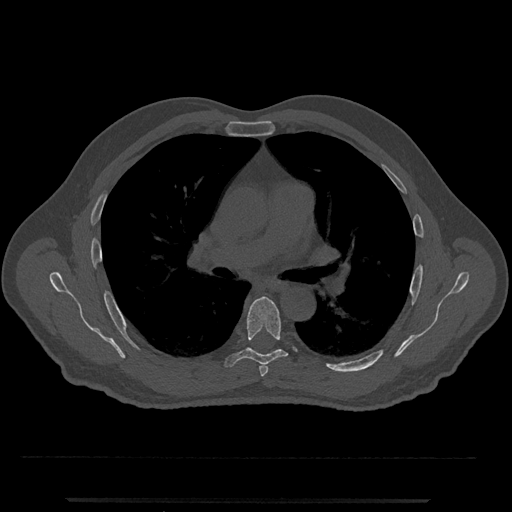
CT including the spine, one axial slice. Slice 741 of 797 in the series (ordered by position). Reconstruction kernel Br40s/3. 120 kVp. Bone window (W 1800 / L 400 HU). 512 × 512 image matrix. Male patient, age 63 years. From the clinical record (not read from this slice): primary cancer: prostate.
Outlined on this slice (semi-automatic segmentation, software-assisted and operator-edited):
- T5 vertebra: bounding box [x1, y1, x2, y2] px = [259, 364, 268, 377]
- T6 vertebra: [225, 296, 288, 367]